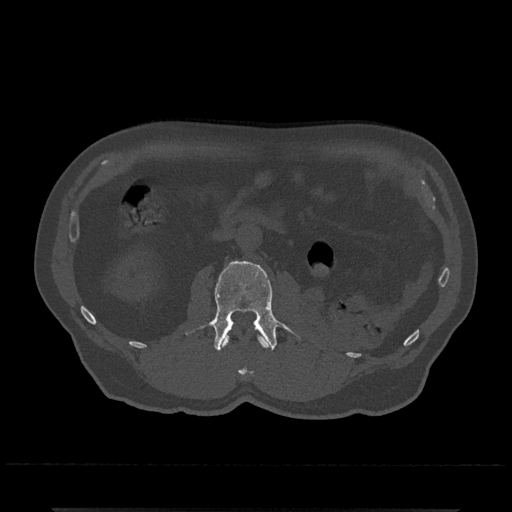
CT including the spine, one axial slice. Position 305 of 797 along the scan axis. Reconstruction kernel Br40s/3. Bone window (W 1800 / L 400 HU). 512 × 512 image matrix, field of view 393 × 393 mm. Patient: male, 67 years. Case-level facts recorded for this patient, not image findings: primary cancer: prostate.
Annotated regions visible in this slice (semi-automatically segmented with operator editing):
- L1 vertebra: bounding box [x1, y1, x2, y2] px = [222, 334, 269, 376]
- L2 vertebra: [186, 261, 293, 351]